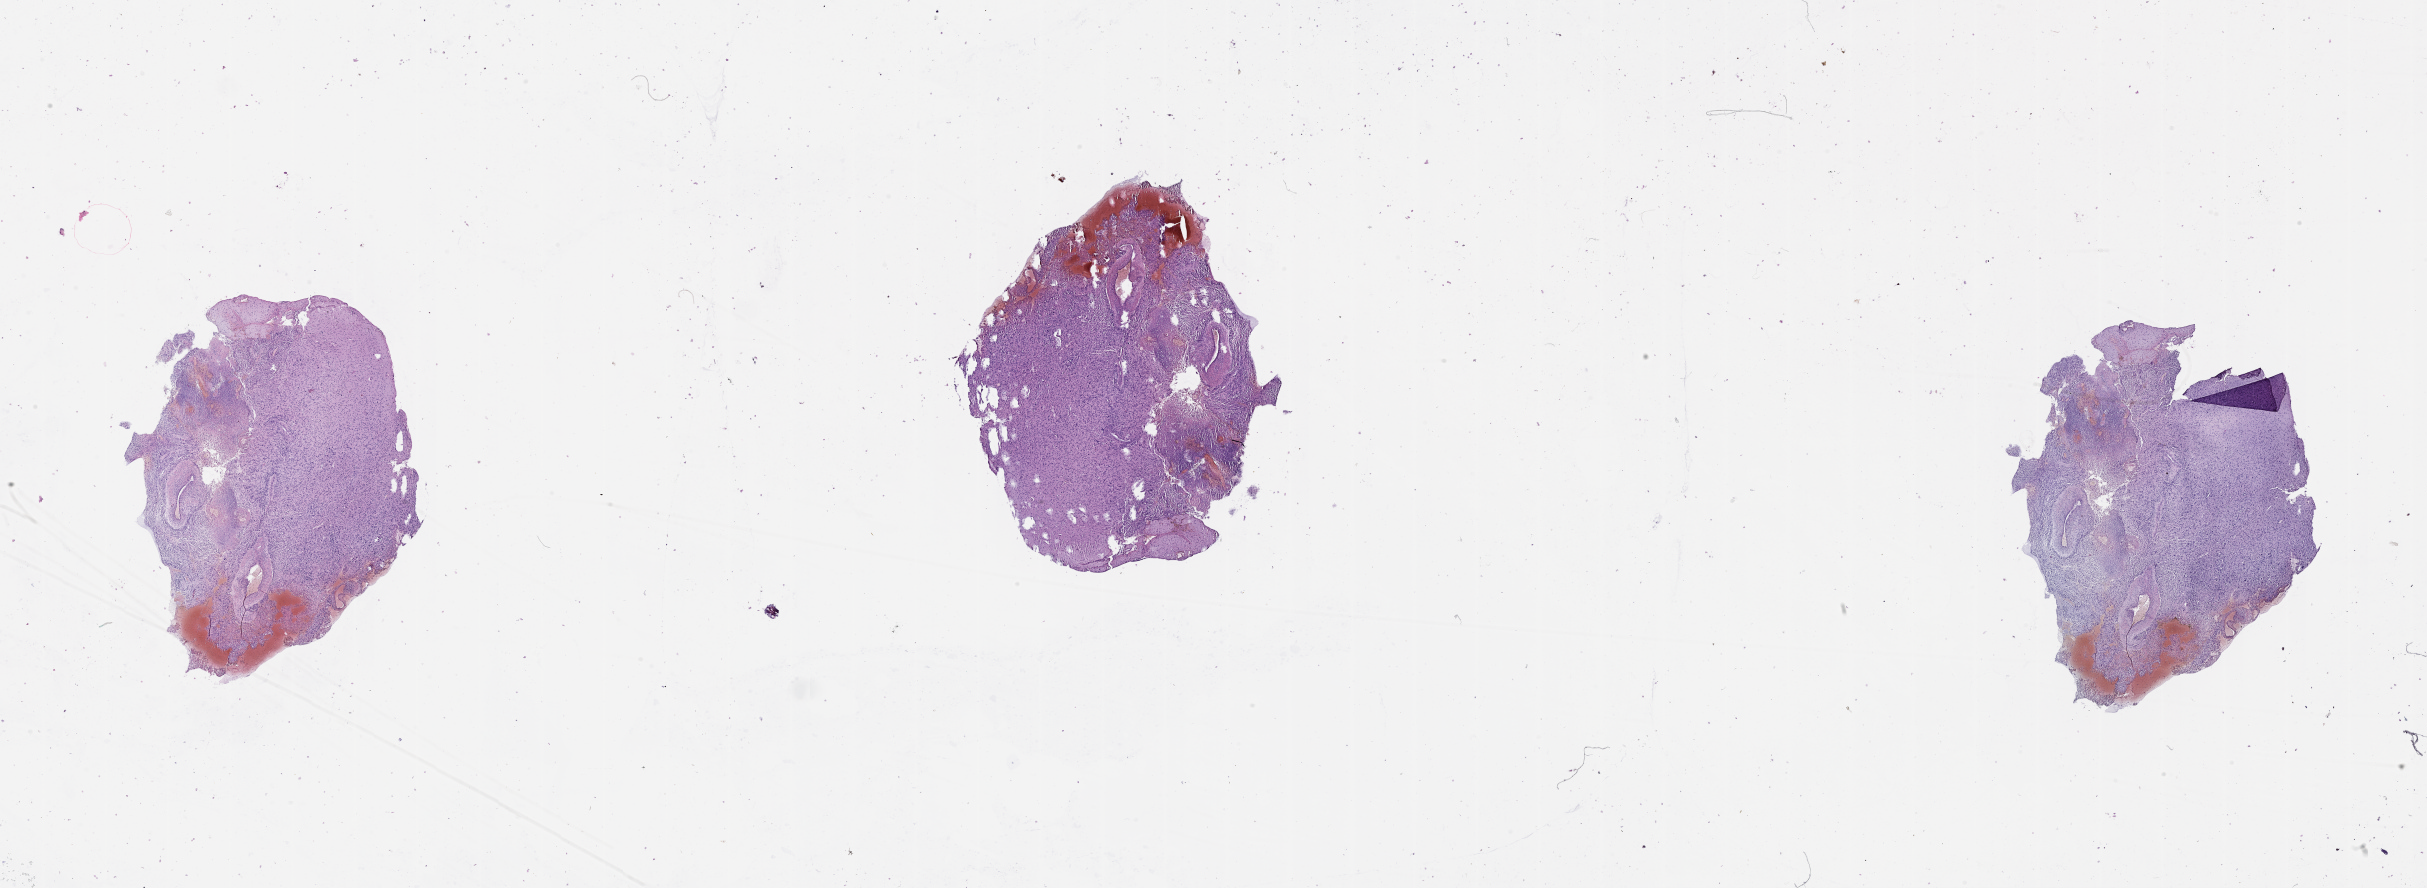
Whole-slide histology image, H&E-stained, low-resolution overview of the scanned area, about 39.1 x 14.3 mm (slide scanned at 20x), tumour tissue sample, brain. Male, 63 y/o.
Diagnosis: Glioblastoma.